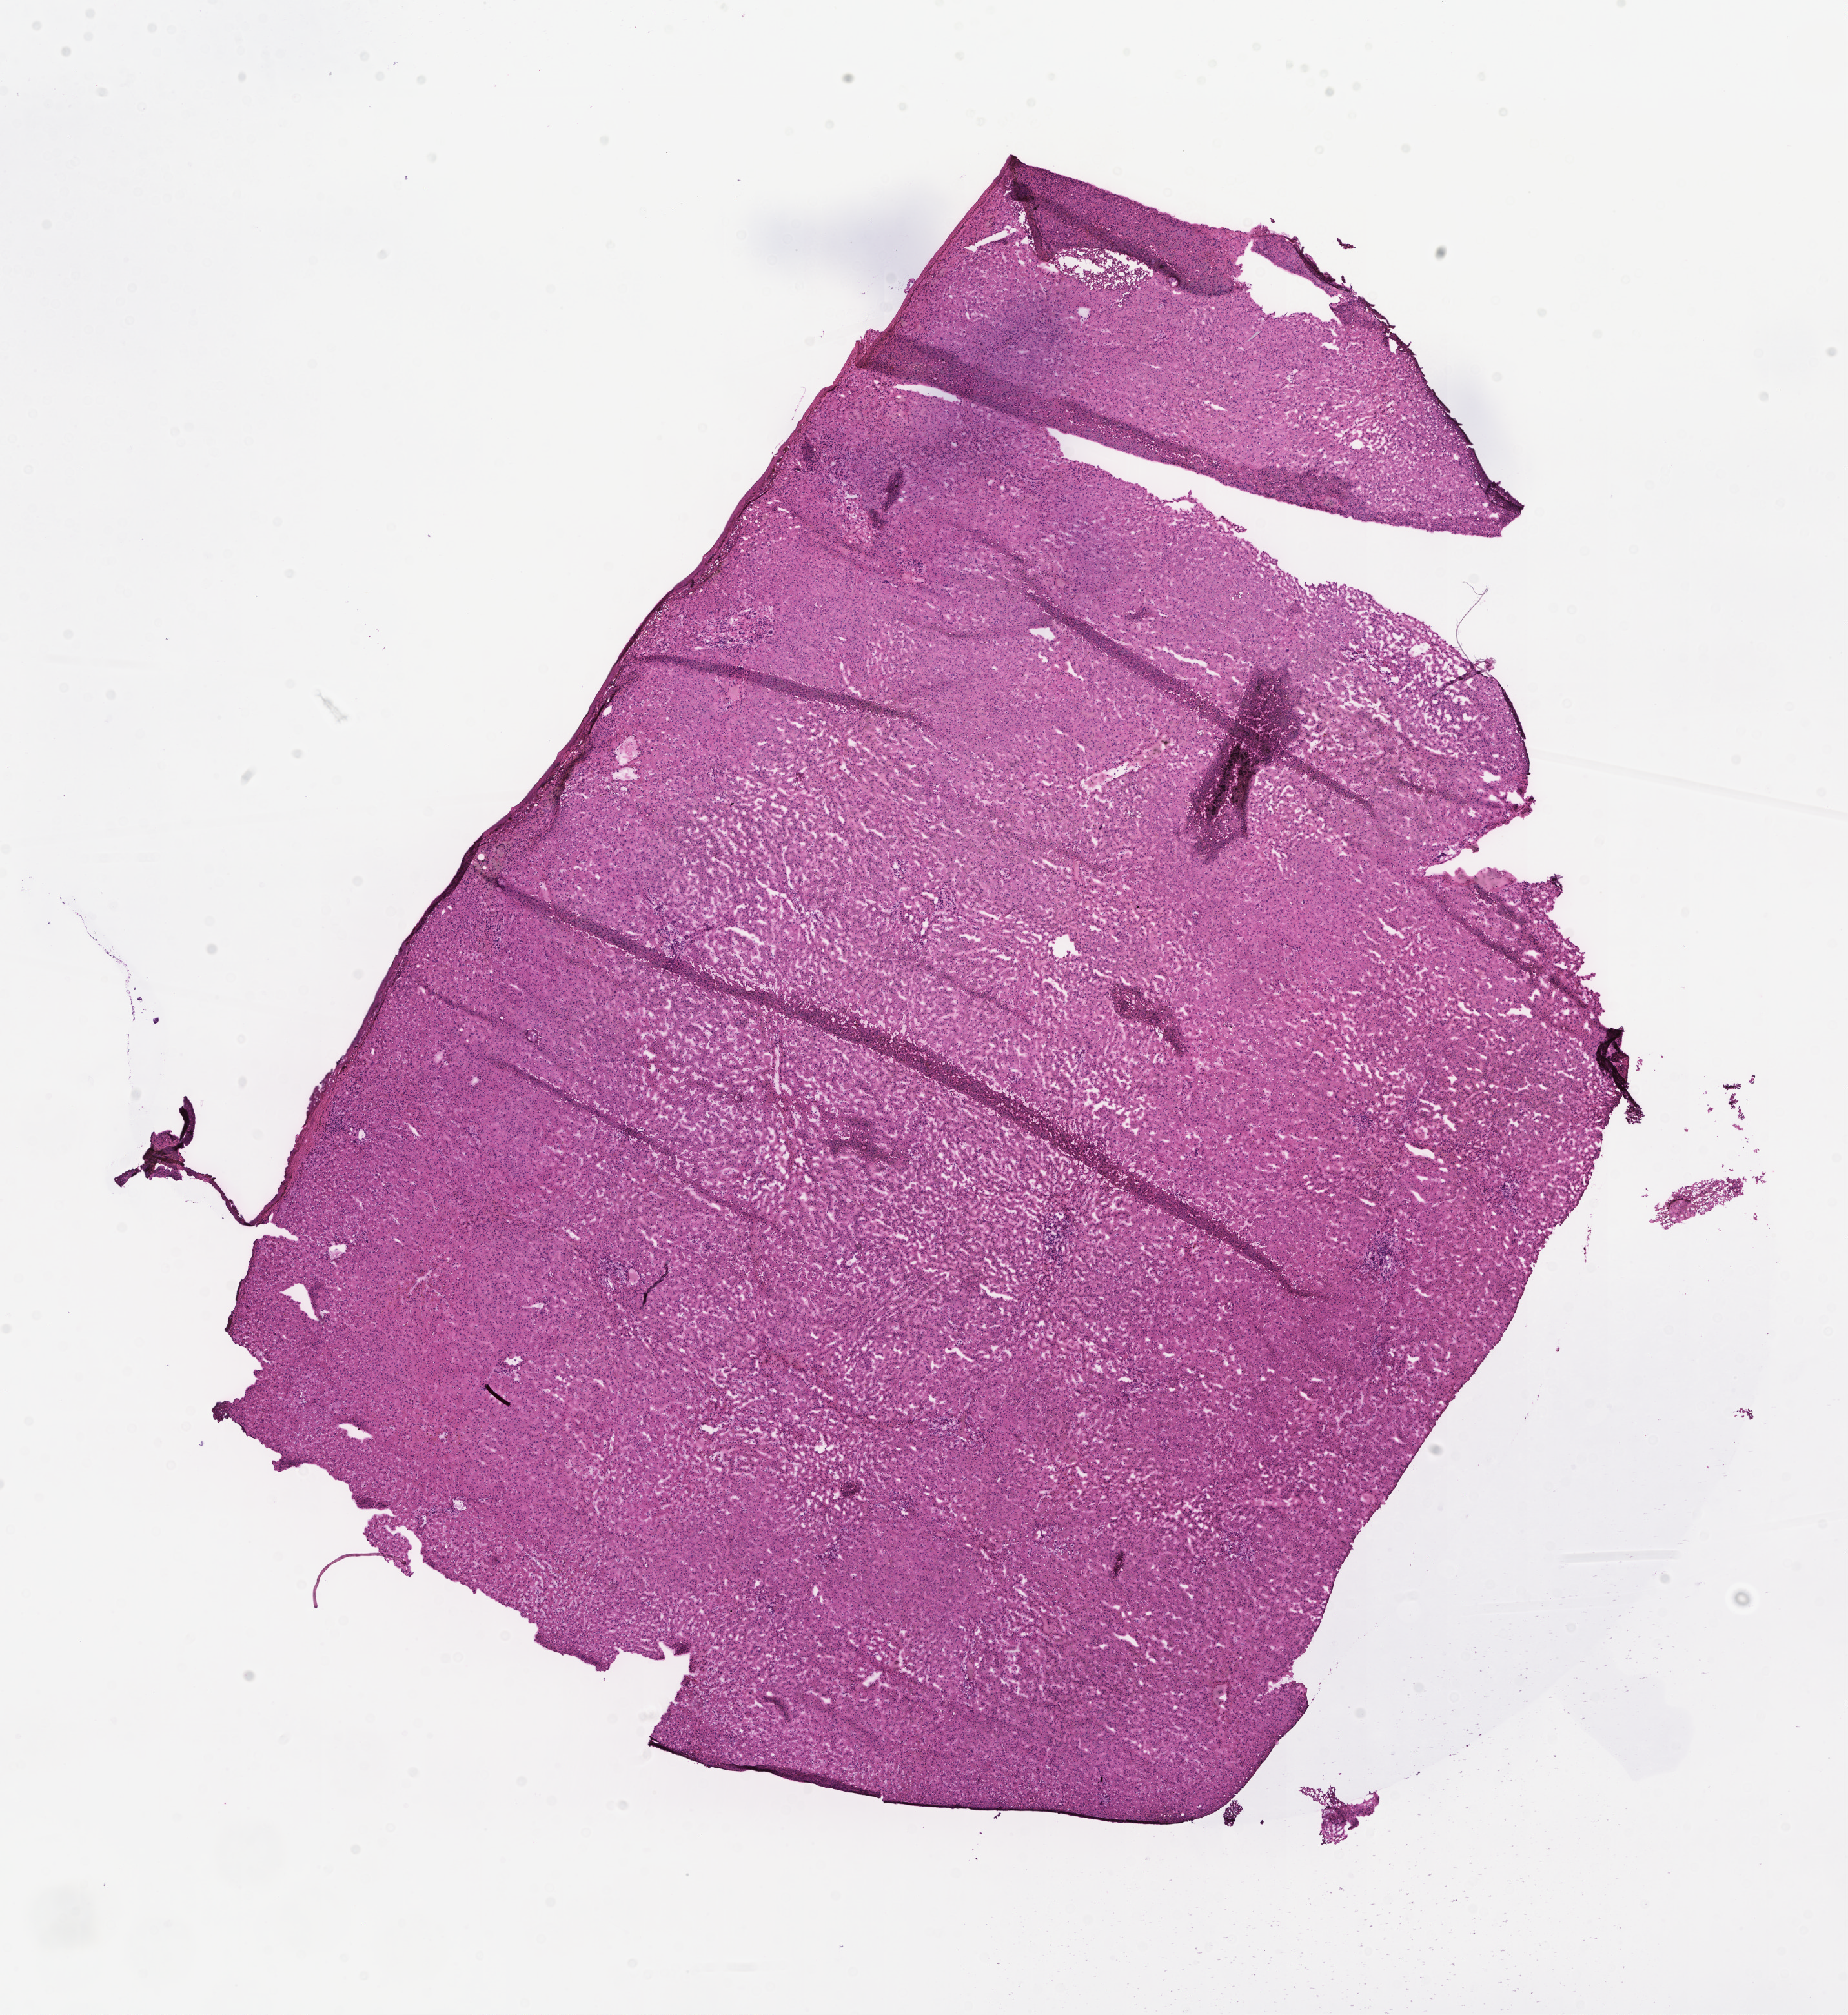
Whole-slide image, H&E stain — a low-resolution overview of the entire scanned area, about 11.6 x 12.6 mm; frozen section; specimen: non-tumor (normal tissue) sample from a patient with adenocarcinoma, NOS; anatomic site: rectum. Patient: male, age at initial diagnosis 71 years. Slide review estimates, as recorded: tumor cells 0%, tumor nuclei 0%, stromal cells 0%, necrosis 0%, normal cells 100%. Infiltration values recorded for this section: lymphocyte infiltration 5%, monocyte infiltration 0%, neutrophil infiltration 0%.
This section: non-tumor tissue sample; the patient's diagnosis is given above.